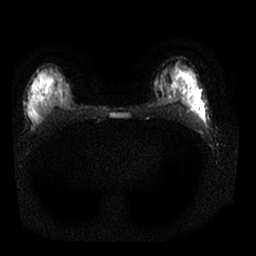
Breast MRI, one axial slice. Diffusion-weighted series; image 2 of 4 stored at this slice position (different b-values; order by instance number). 1.5 T. 4 mm slice thickness. 256 × 256 image matrix, field of view 320 × 320 mm. Female patient.
Outlined on this slice (outlined manually by an expert reader):
- tumour on diffusion-weighted imaging: bounding box (x1, y1, x2, y2) in pixels: (192, 102, 199, 105)